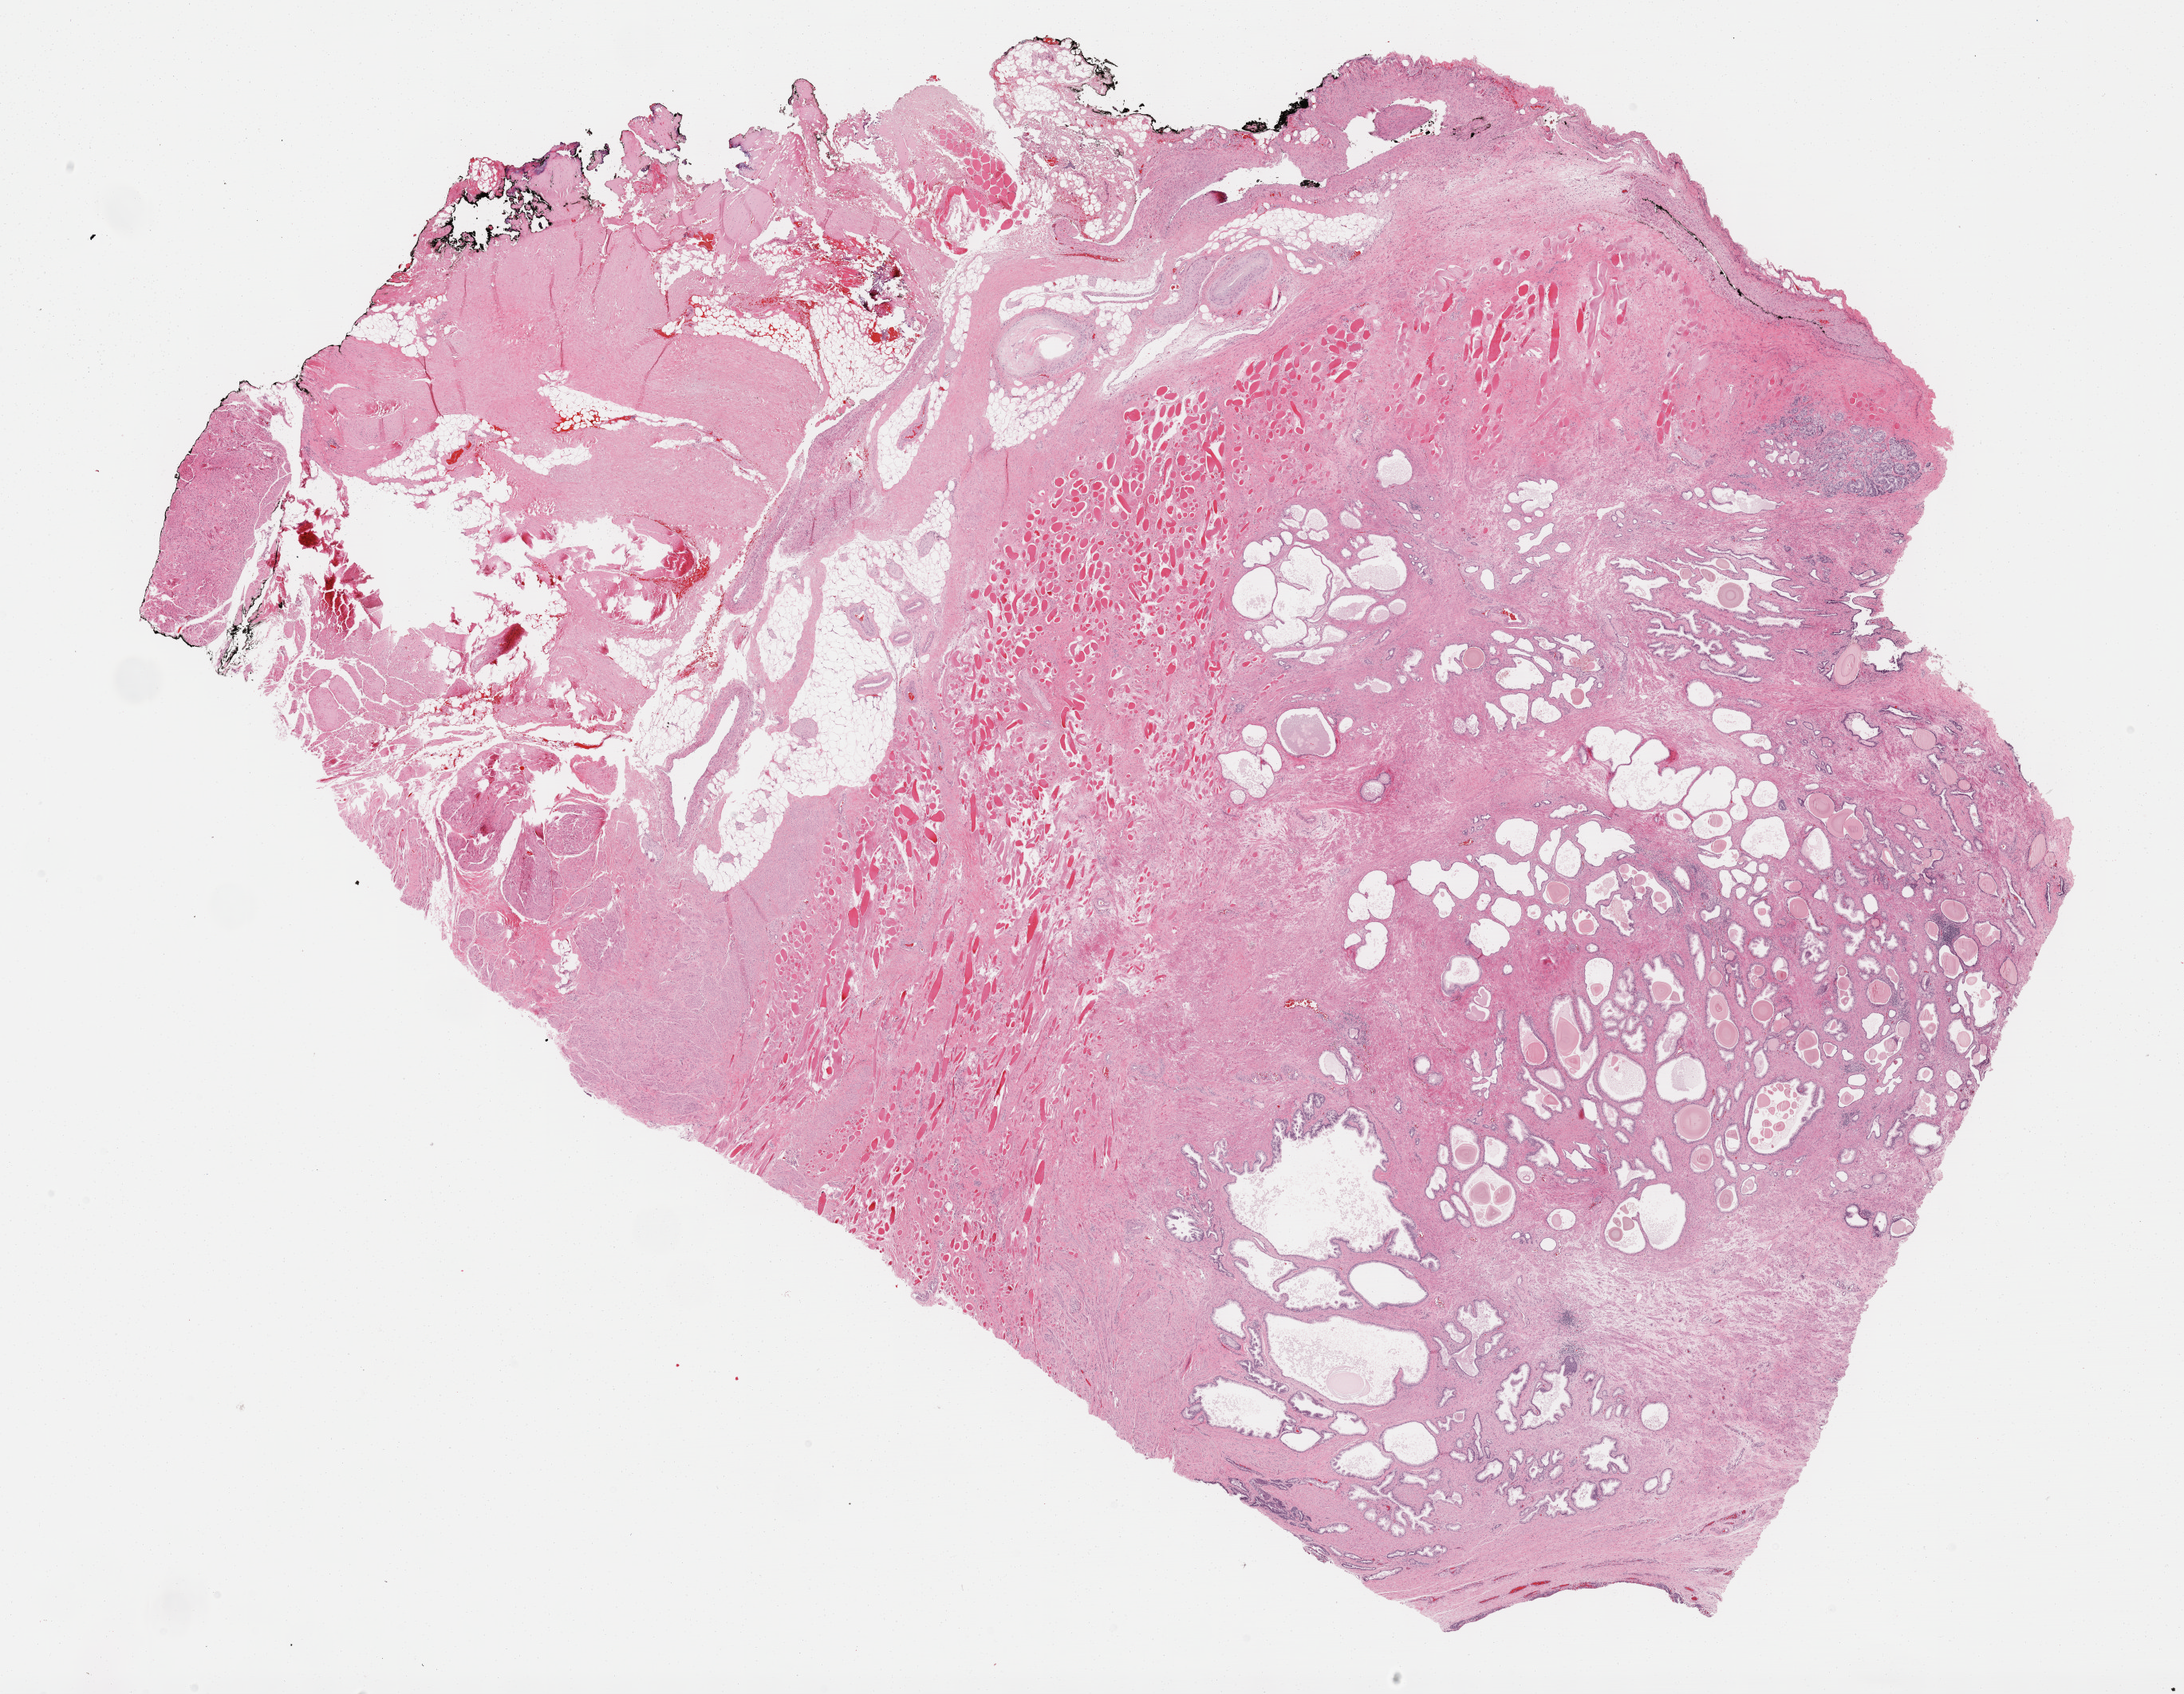
Whole-slide histology image, H&E-stained, shown as a low-resolution overview of the whole scanned area (about 22.1 x 17.2 mm, acquisition: 40x scan); formalin-fixed paraffin-embedded (FFPE) diagnostic section; prostate, primary tumour sample. Male, age 65 years at initial diagnosis. Gleason score: 9 (4+5).
Lymph nodes positive (case pathology): 0 of 3 examined. Diagnosis: Adenocarcinoma, NOS. Laterality: right.